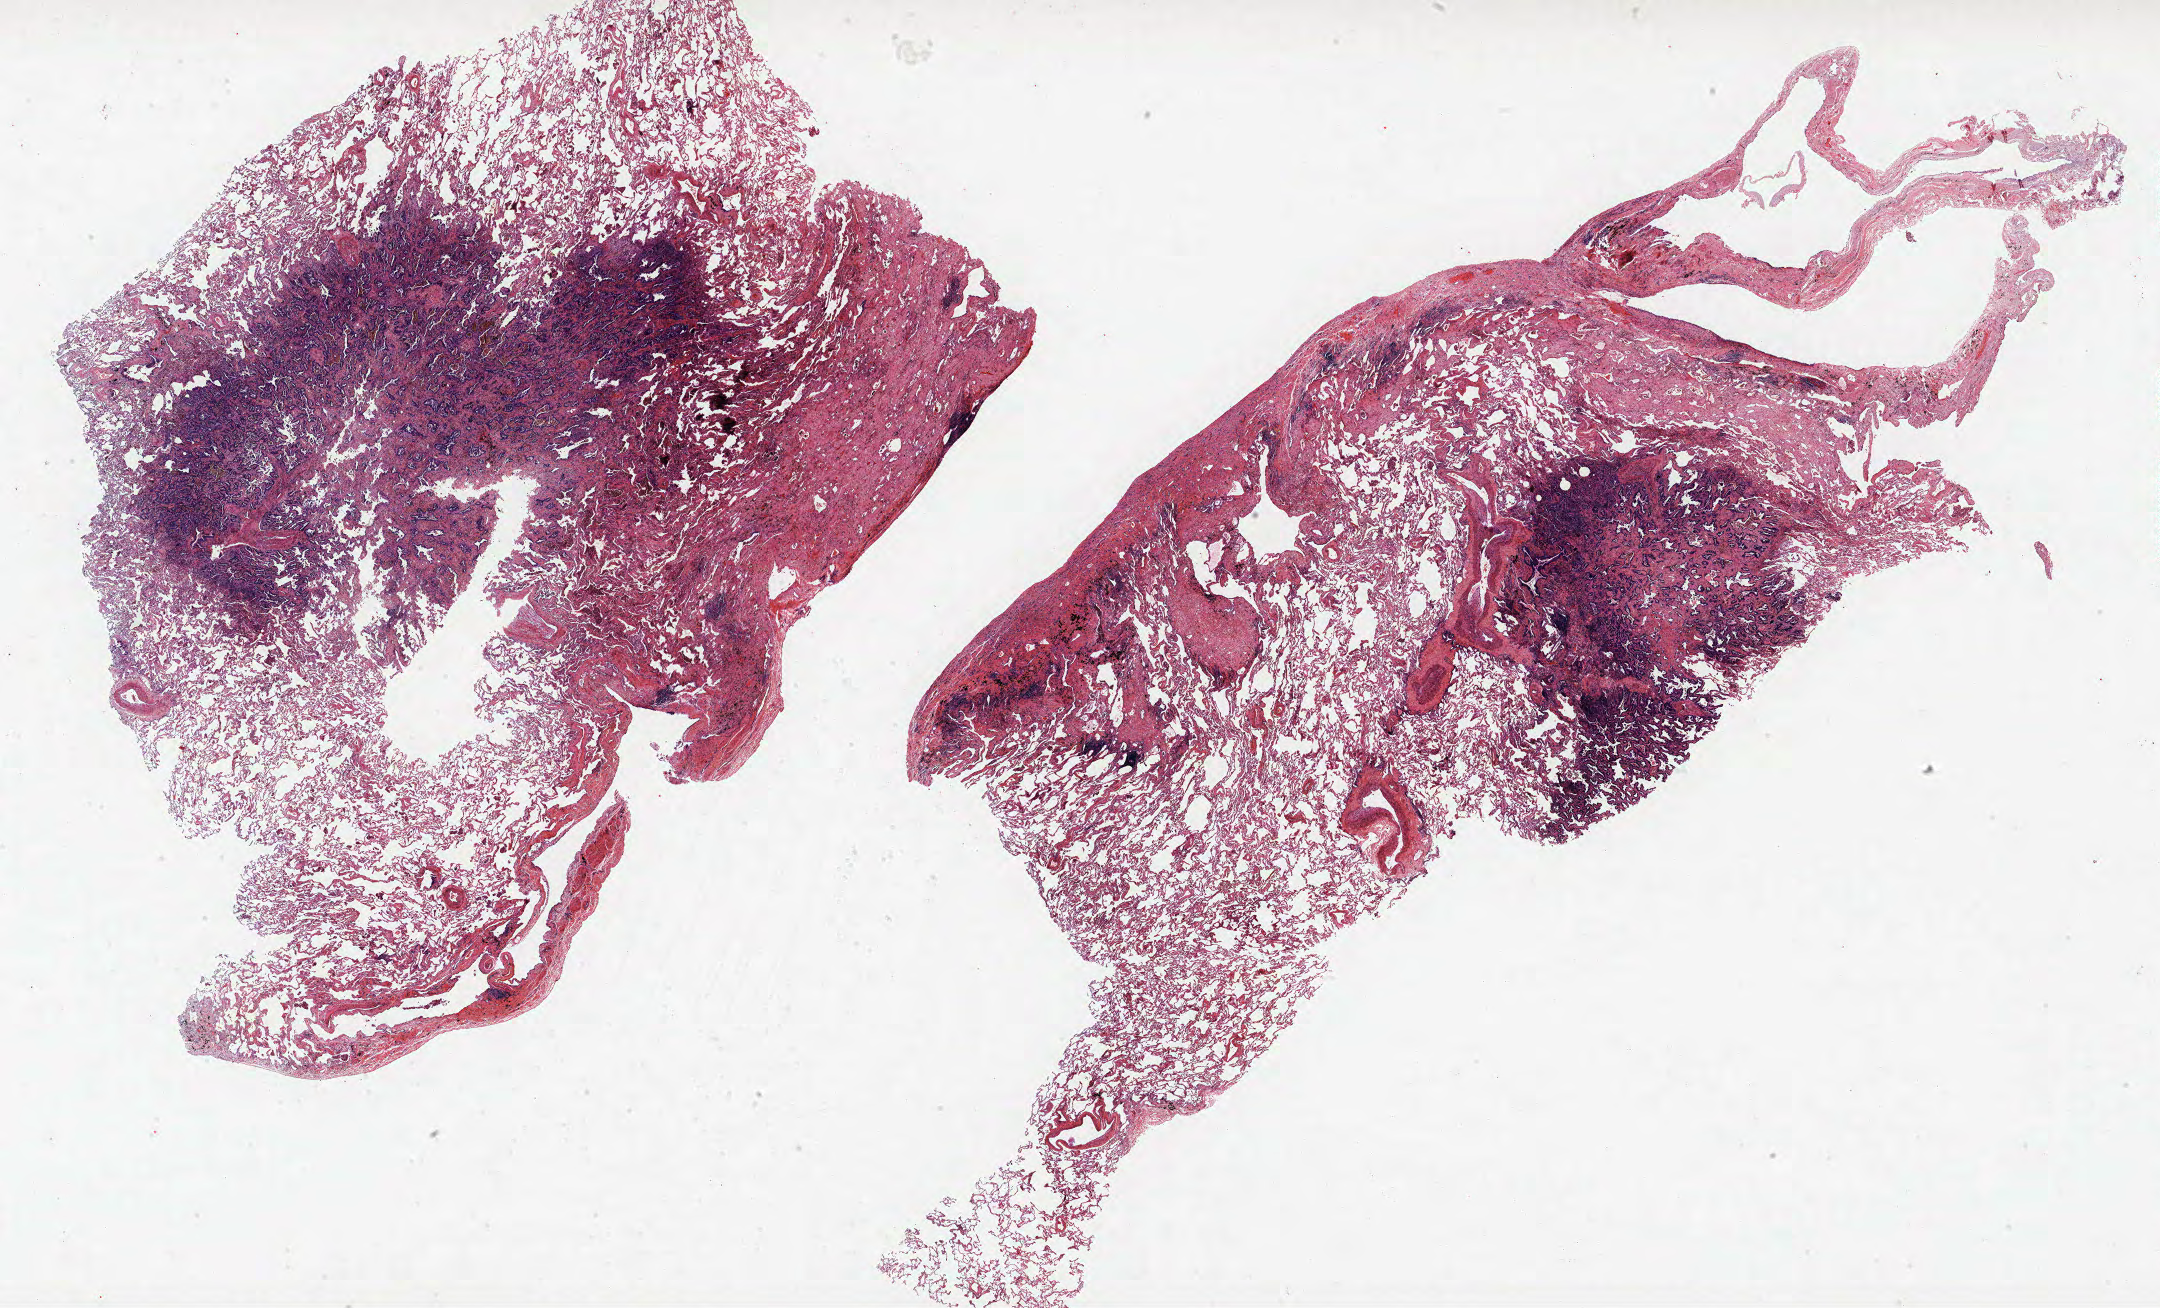
H&E-stained whole-slide image, low-resolution overview of the scanned area, about 34.6 x 20.9 mm, formalin-fixed paraffin-embedded (FFPE) section, lung tissue. Male, age 62 at enrolment. Current smoker at enrolment. Grade: well differentiated (G1).
Primary tumour location (clinical record): left upper lobe. Stage (AJCC 6th edition): IB. Tumour size (pathology): 17 mm. ICD-O-3 topography: upper lobe of lung (C34.1). Participant's lung-cancer diagnosis: Adenocarcinoma, NOS.